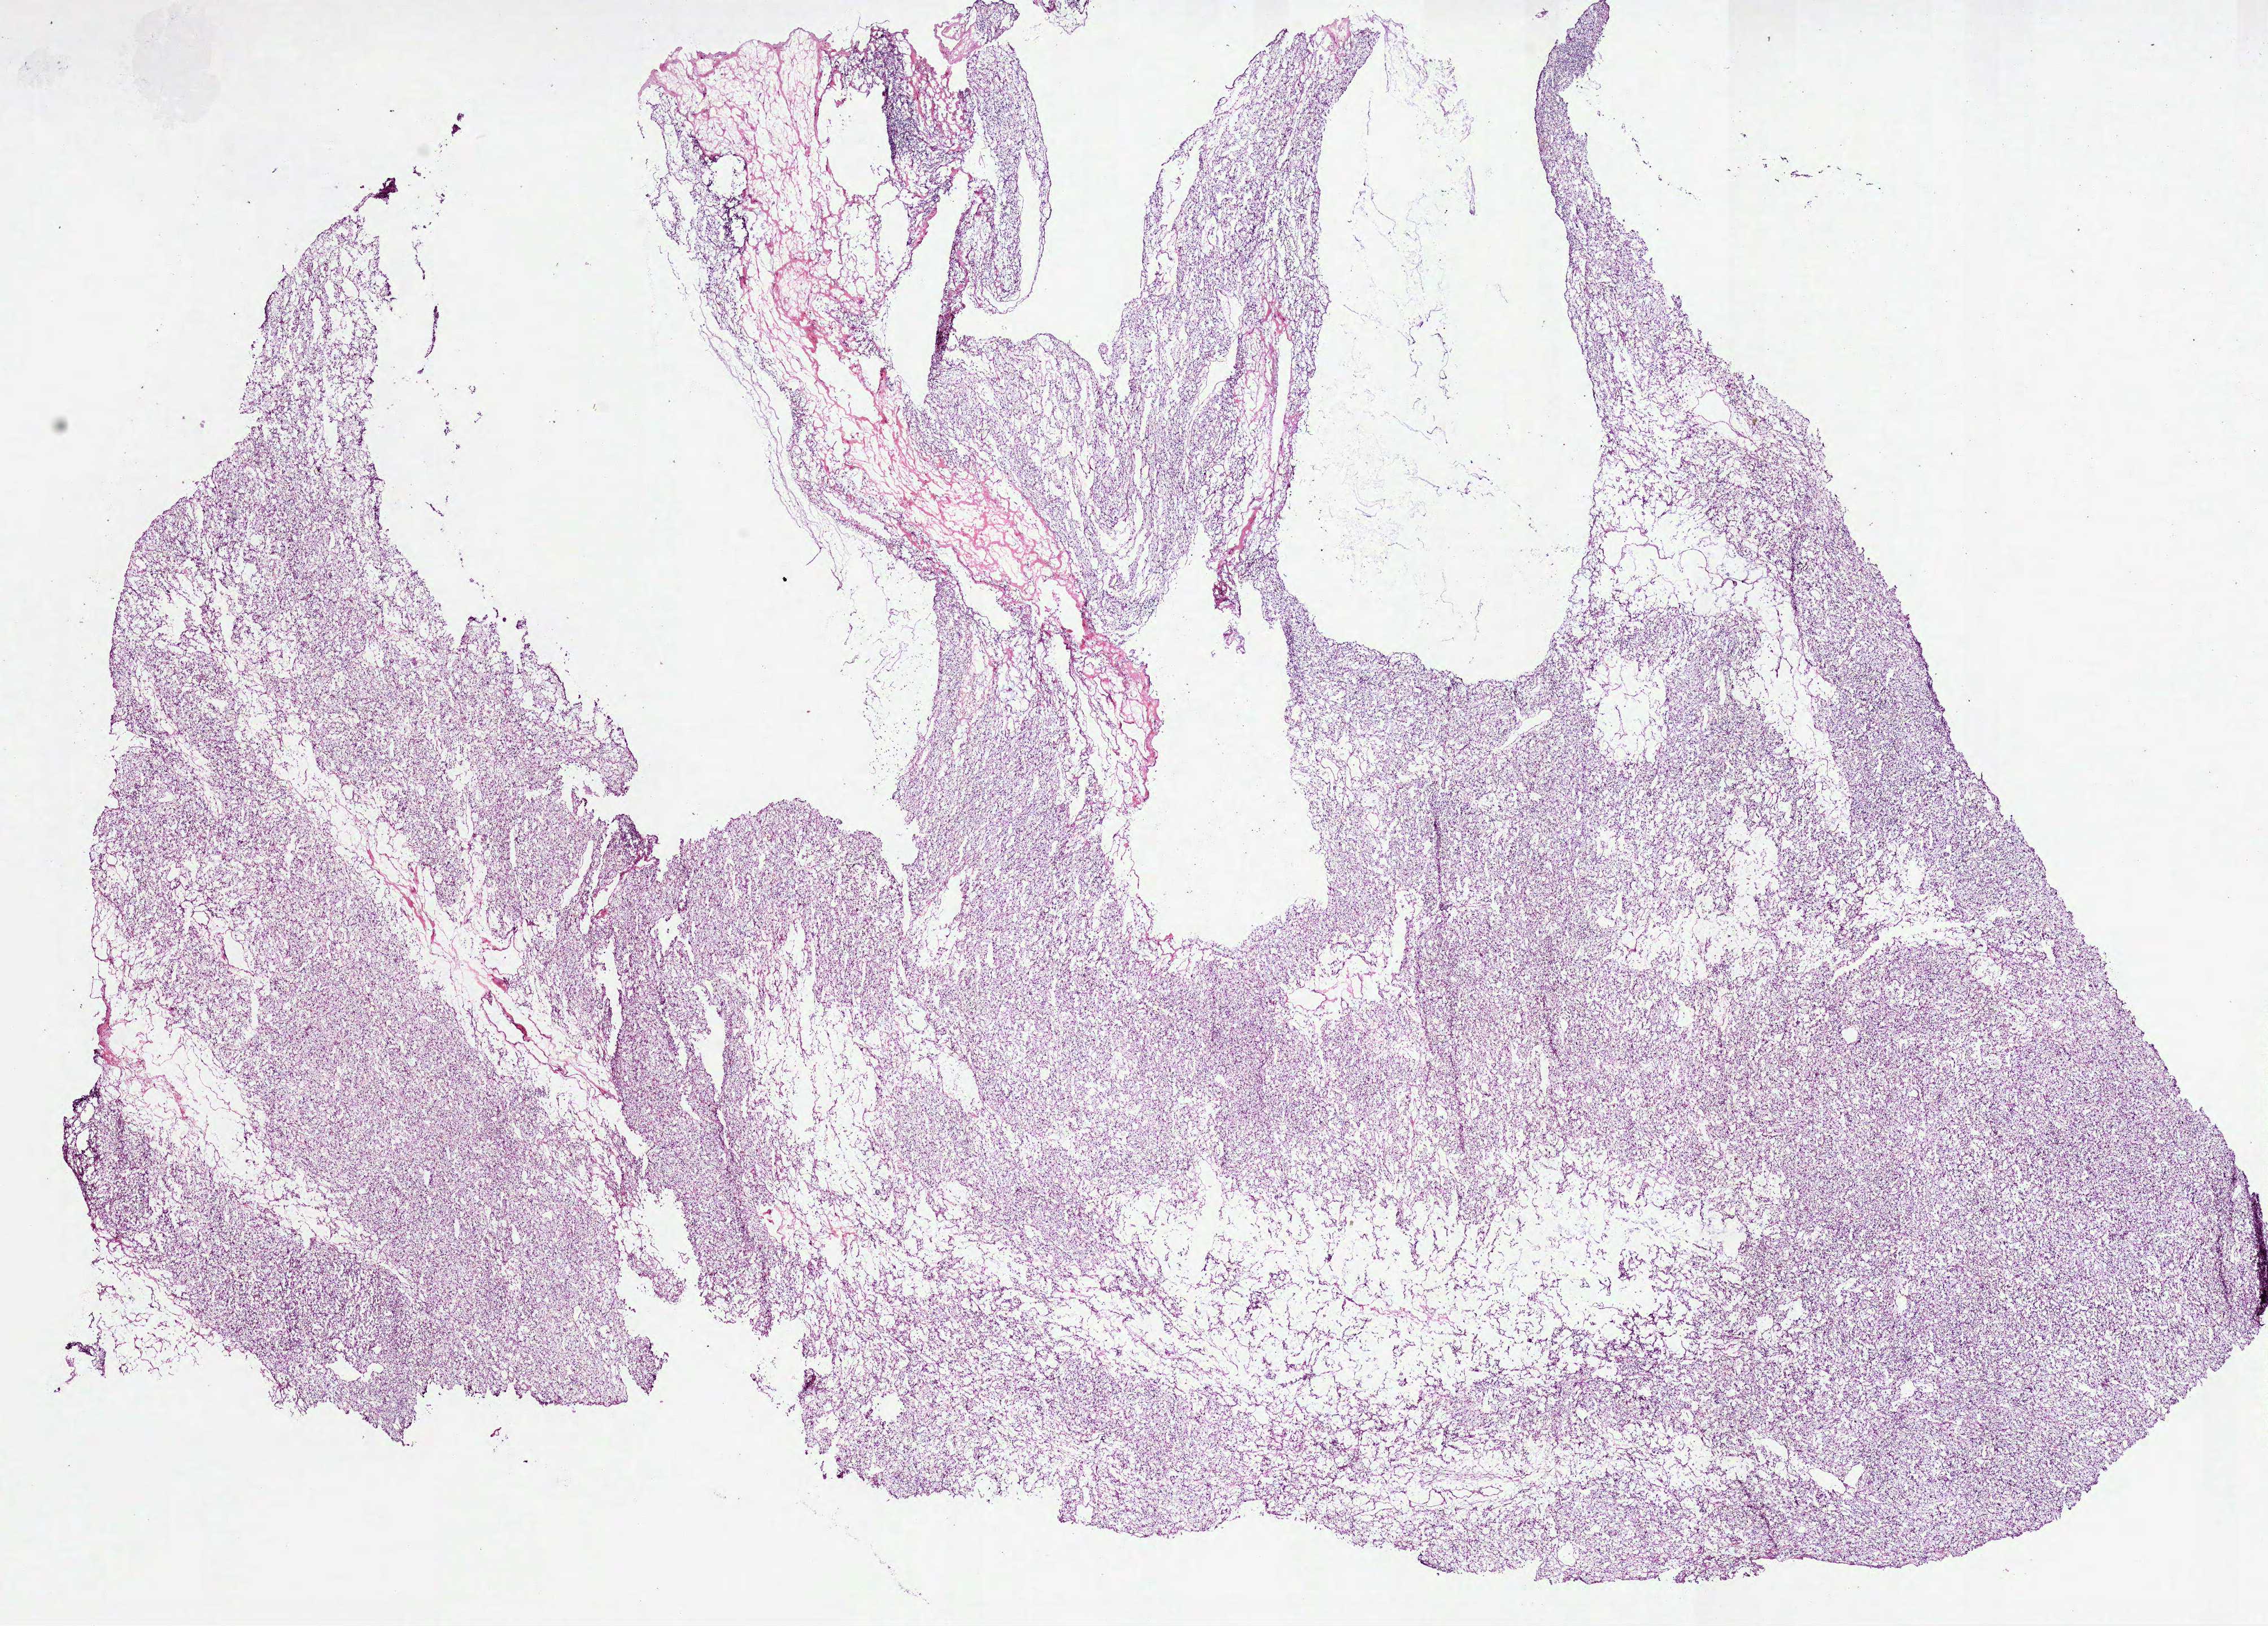
H&E-stained whole-slide image — a low-resolution overview of the entire scanned area, about 16.2 x 11.6 mm. Frozen section. Primary tumour sample from the kidney. Male patient; age at initial diagnosis 60 years. Histologic grade: G2 (moderately differentiated). Slide review estimates, as recorded: tumour cells 90%, tumour nuclei 85%, normal cells 0%, stromal cells 10%, necrosis 0%.
Histologic diagnosis: Clear cell adenocarcinoma, NOS. TNM: T2 N0 M0. AJCC pathologic stage: II. Laterality: right.